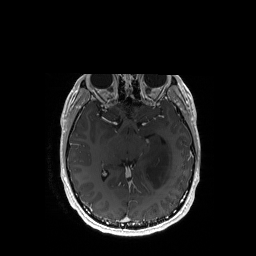
Brain MRI from a brain-tumour surgery series, one axial slice. Slice 99 of 192 in the series (ordered by position). T1-weighted post-contrast. 1 mm slice thickness. 256 × 256 image matrix, field of view 256 × 256 mm. Case-level facts recorded for this patient, not image findings: histopathology: Astrocytoma; WHO grade: 3; IDH mutation: yes.
Structures marked on this image (manually delineated by an expert):
- tumour: box from (x=145, y=144) to (x=171, y=188) px